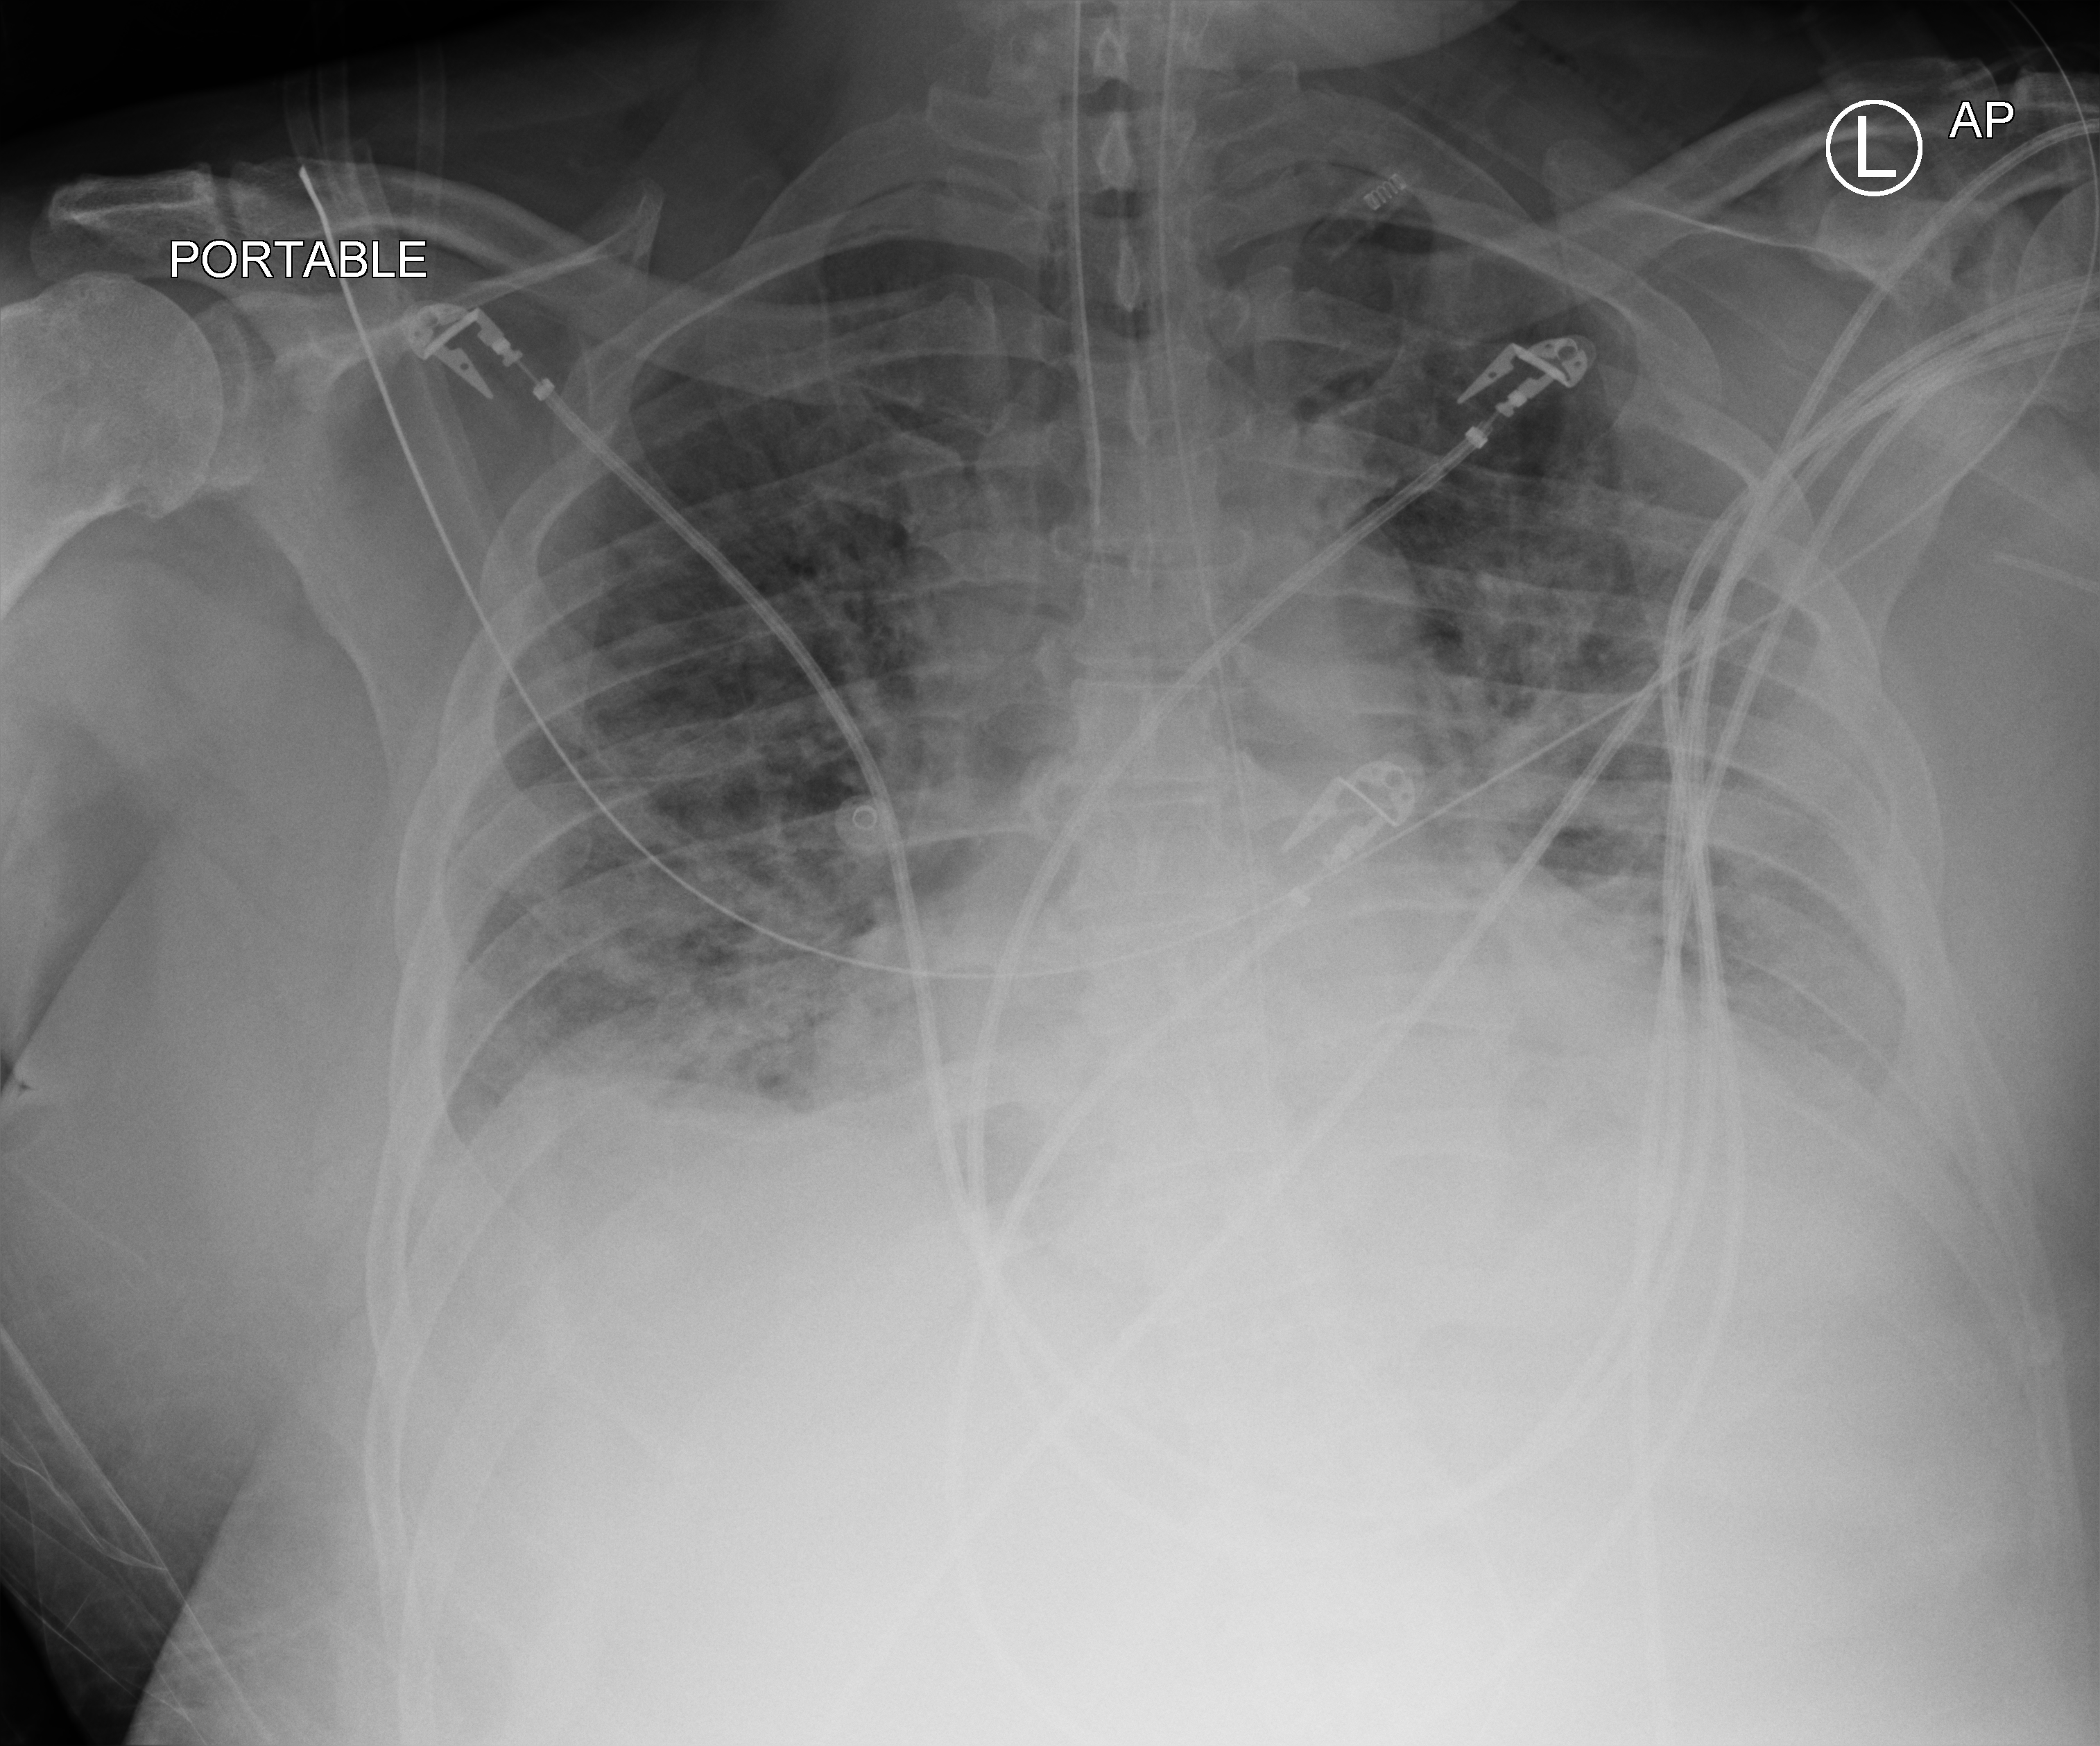
Bedside chest radiograph (computed radiography). Male patient hospitalised with COVID-19, age 18–59 years.
Admission-level facts for this patient (not findings on this image; timing relative to this image not recorded): admitted to intensive care during this hospital stay: yes; mechanically ventilated during this hospital stay: yes; chronic kidney disease (admission record): no.